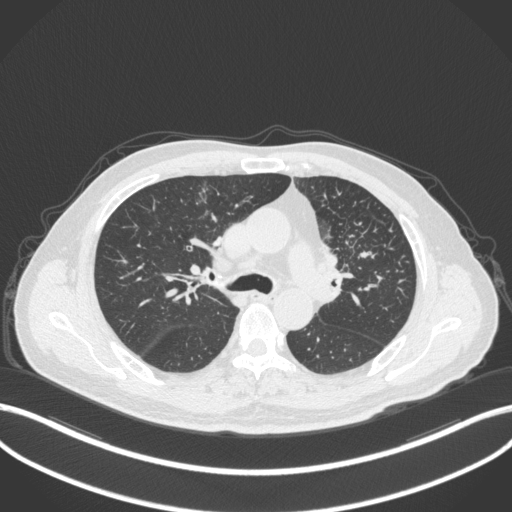
Chest CT, one axial slice; slice 224 of 386 in the series (ordered by position); reconstruction kernel B31f; 120 kVp; lung window (W 1500 / L -600 HU); 1 mm slice thickness; 512 × 512 image matrix. Patient: male, 69 years. From the clinical record (not read from this slice): clinical TNM (as recorded): T2a N2 M0; histopathological grade: G2-3.
Outlined on this slice (rectangle marked by the reading radiologist):
- lung tumour (recorded histology: adenocarcinoma): bounding box [x1, y1, x2, y2] px = [315, 240, 349, 286]